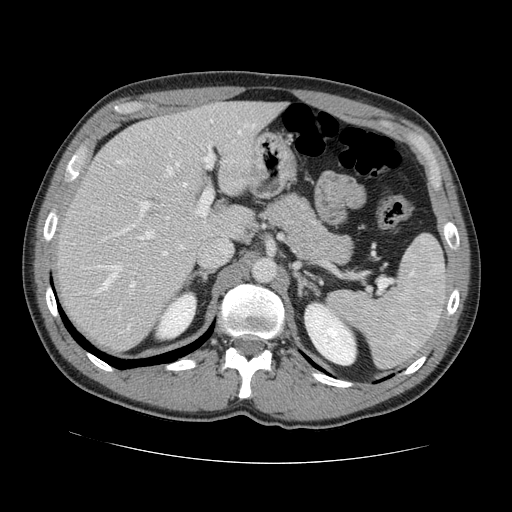
Contrast-enhanced abdominal CT, one axial slice. Slice 88 of 131 in the series (ordered by position). 120 kVp. Intravenous contrast given. Soft-tissue window (W 400 / L 40 HU). 512 × 512 image matrix, field of view 380 × 380 mm. Male patient, age 40 years. From the clinical record (not read from this slice): diagnosis: colorectal cancer liver metastases, imaged before liver resection; multiple liver metastases: yes; largest metastasis: 2.9 cm; disease in both lobes: yes.
Outlined on this slice (expert manual segmentation):
- hepatic veins: bounding box (x1, y1, x2, y2) in pixels: (95, 159, 187, 294)
- liver: (60, 103, 280, 350)
- planned liver remnant (the part of the liver to remain after resection): (102, 103, 281, 237)
- portal vein (with intrahepatic branches): (103, 153, 213, 314)